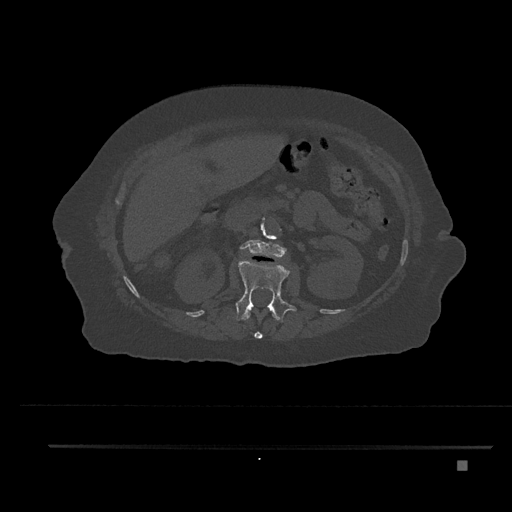
CT including the spine, one axial slice. Slice 221 of 797 in the series (ordered by position). Bone window (W 1800 / L 400 HU). 0.5 mm slice thickness. 512 × 512 image matrix. Female patient, age 76 years. Case-level facts recorded for this patient, not image findings: primary cancer: lung; vertebrae with lytic lesions (as recorded): T11, L3.
Annotated regions visible in this slice (semi-automatically segmented with operator editing):
- L1 vertebra: bounding box [x1, y1, x2, y2] px = [236, 259, 297, 323]
- L2 vertebra: [240, 239, 287, 257]
- T12 vertebra: [245, 311, 276, 339]